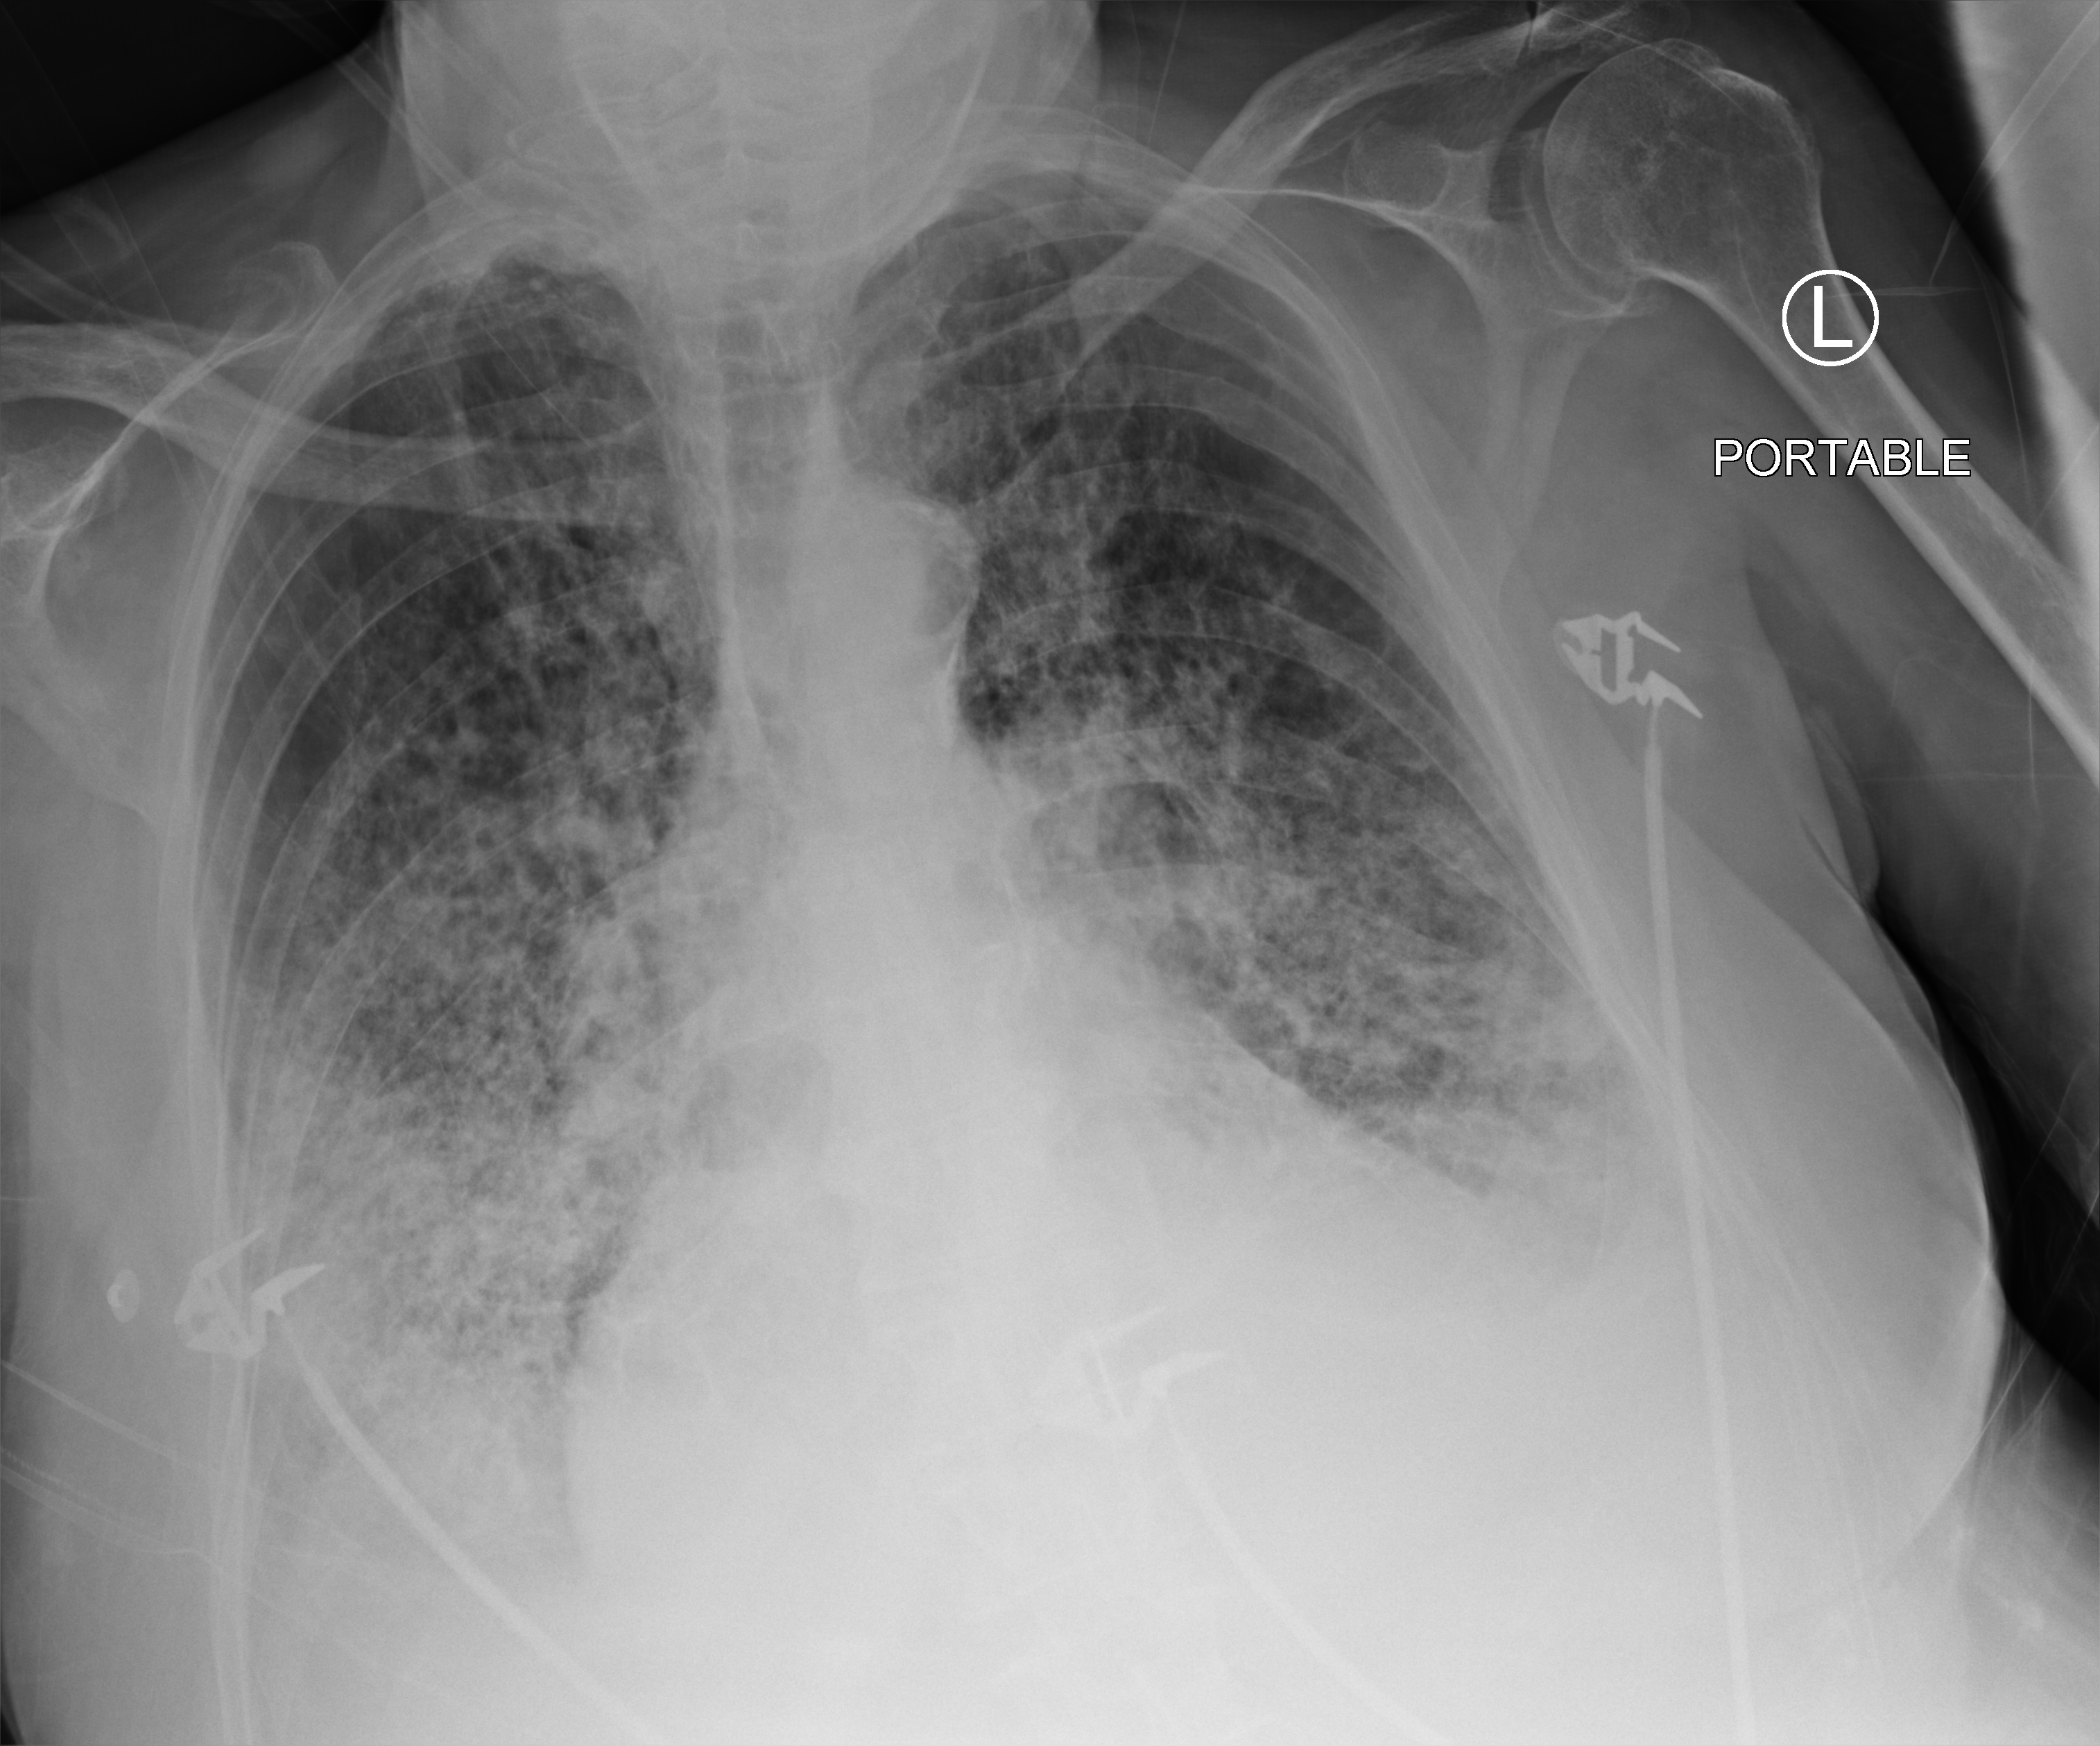
Chest X-ray (portable); anteroposterior (AP) projection. Patient hospitalised with COVID-19; male, aged 75–90 years.
Hospital-stay facts (about this admission, not read from this image; timing relative to this image not recorded): admitted to intensive care during this hospital stay: no.